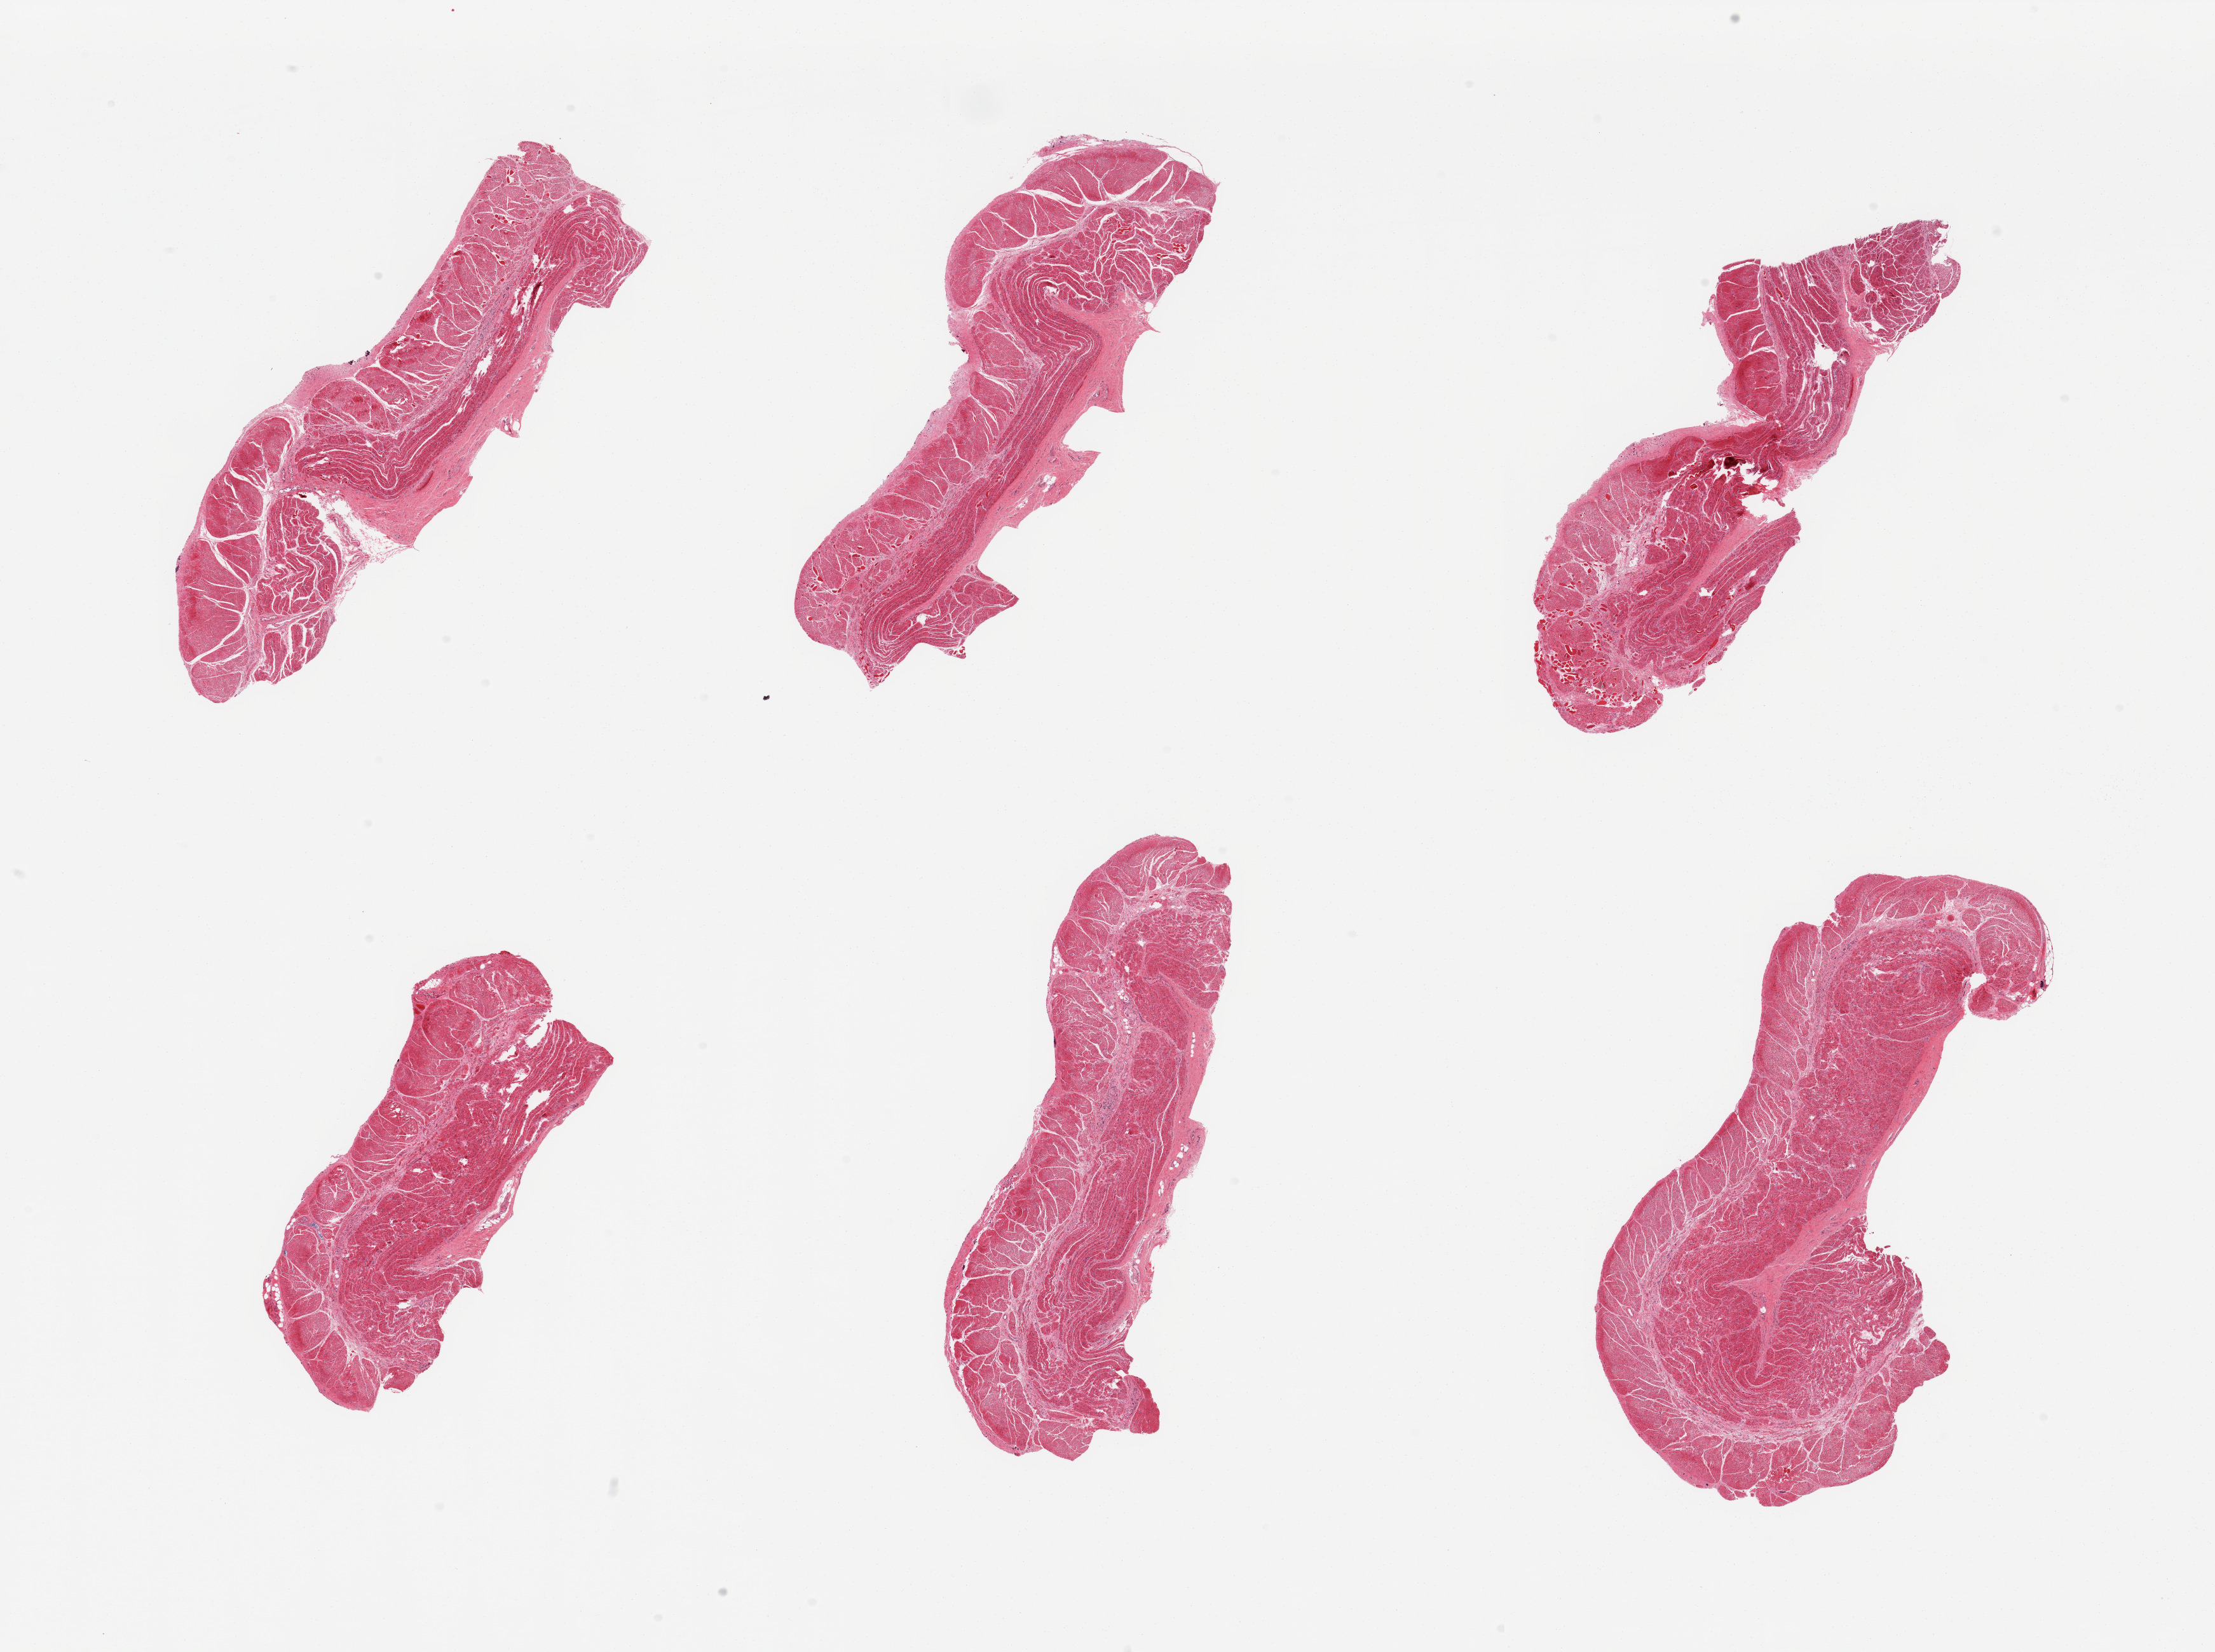
H&E whole-slide image, brightfield, shown as a low-resolution overview of the whole scanned area (about 27.6 x 20.6 mm, from a 20x scan), PAXgene-fixed paraffin-embedded (PFPE) section, section of esophageal muscle (target tissue), tissue donor sample. Male donor.
- review note (as recorded): 6 pieces; well dissected target muscularis